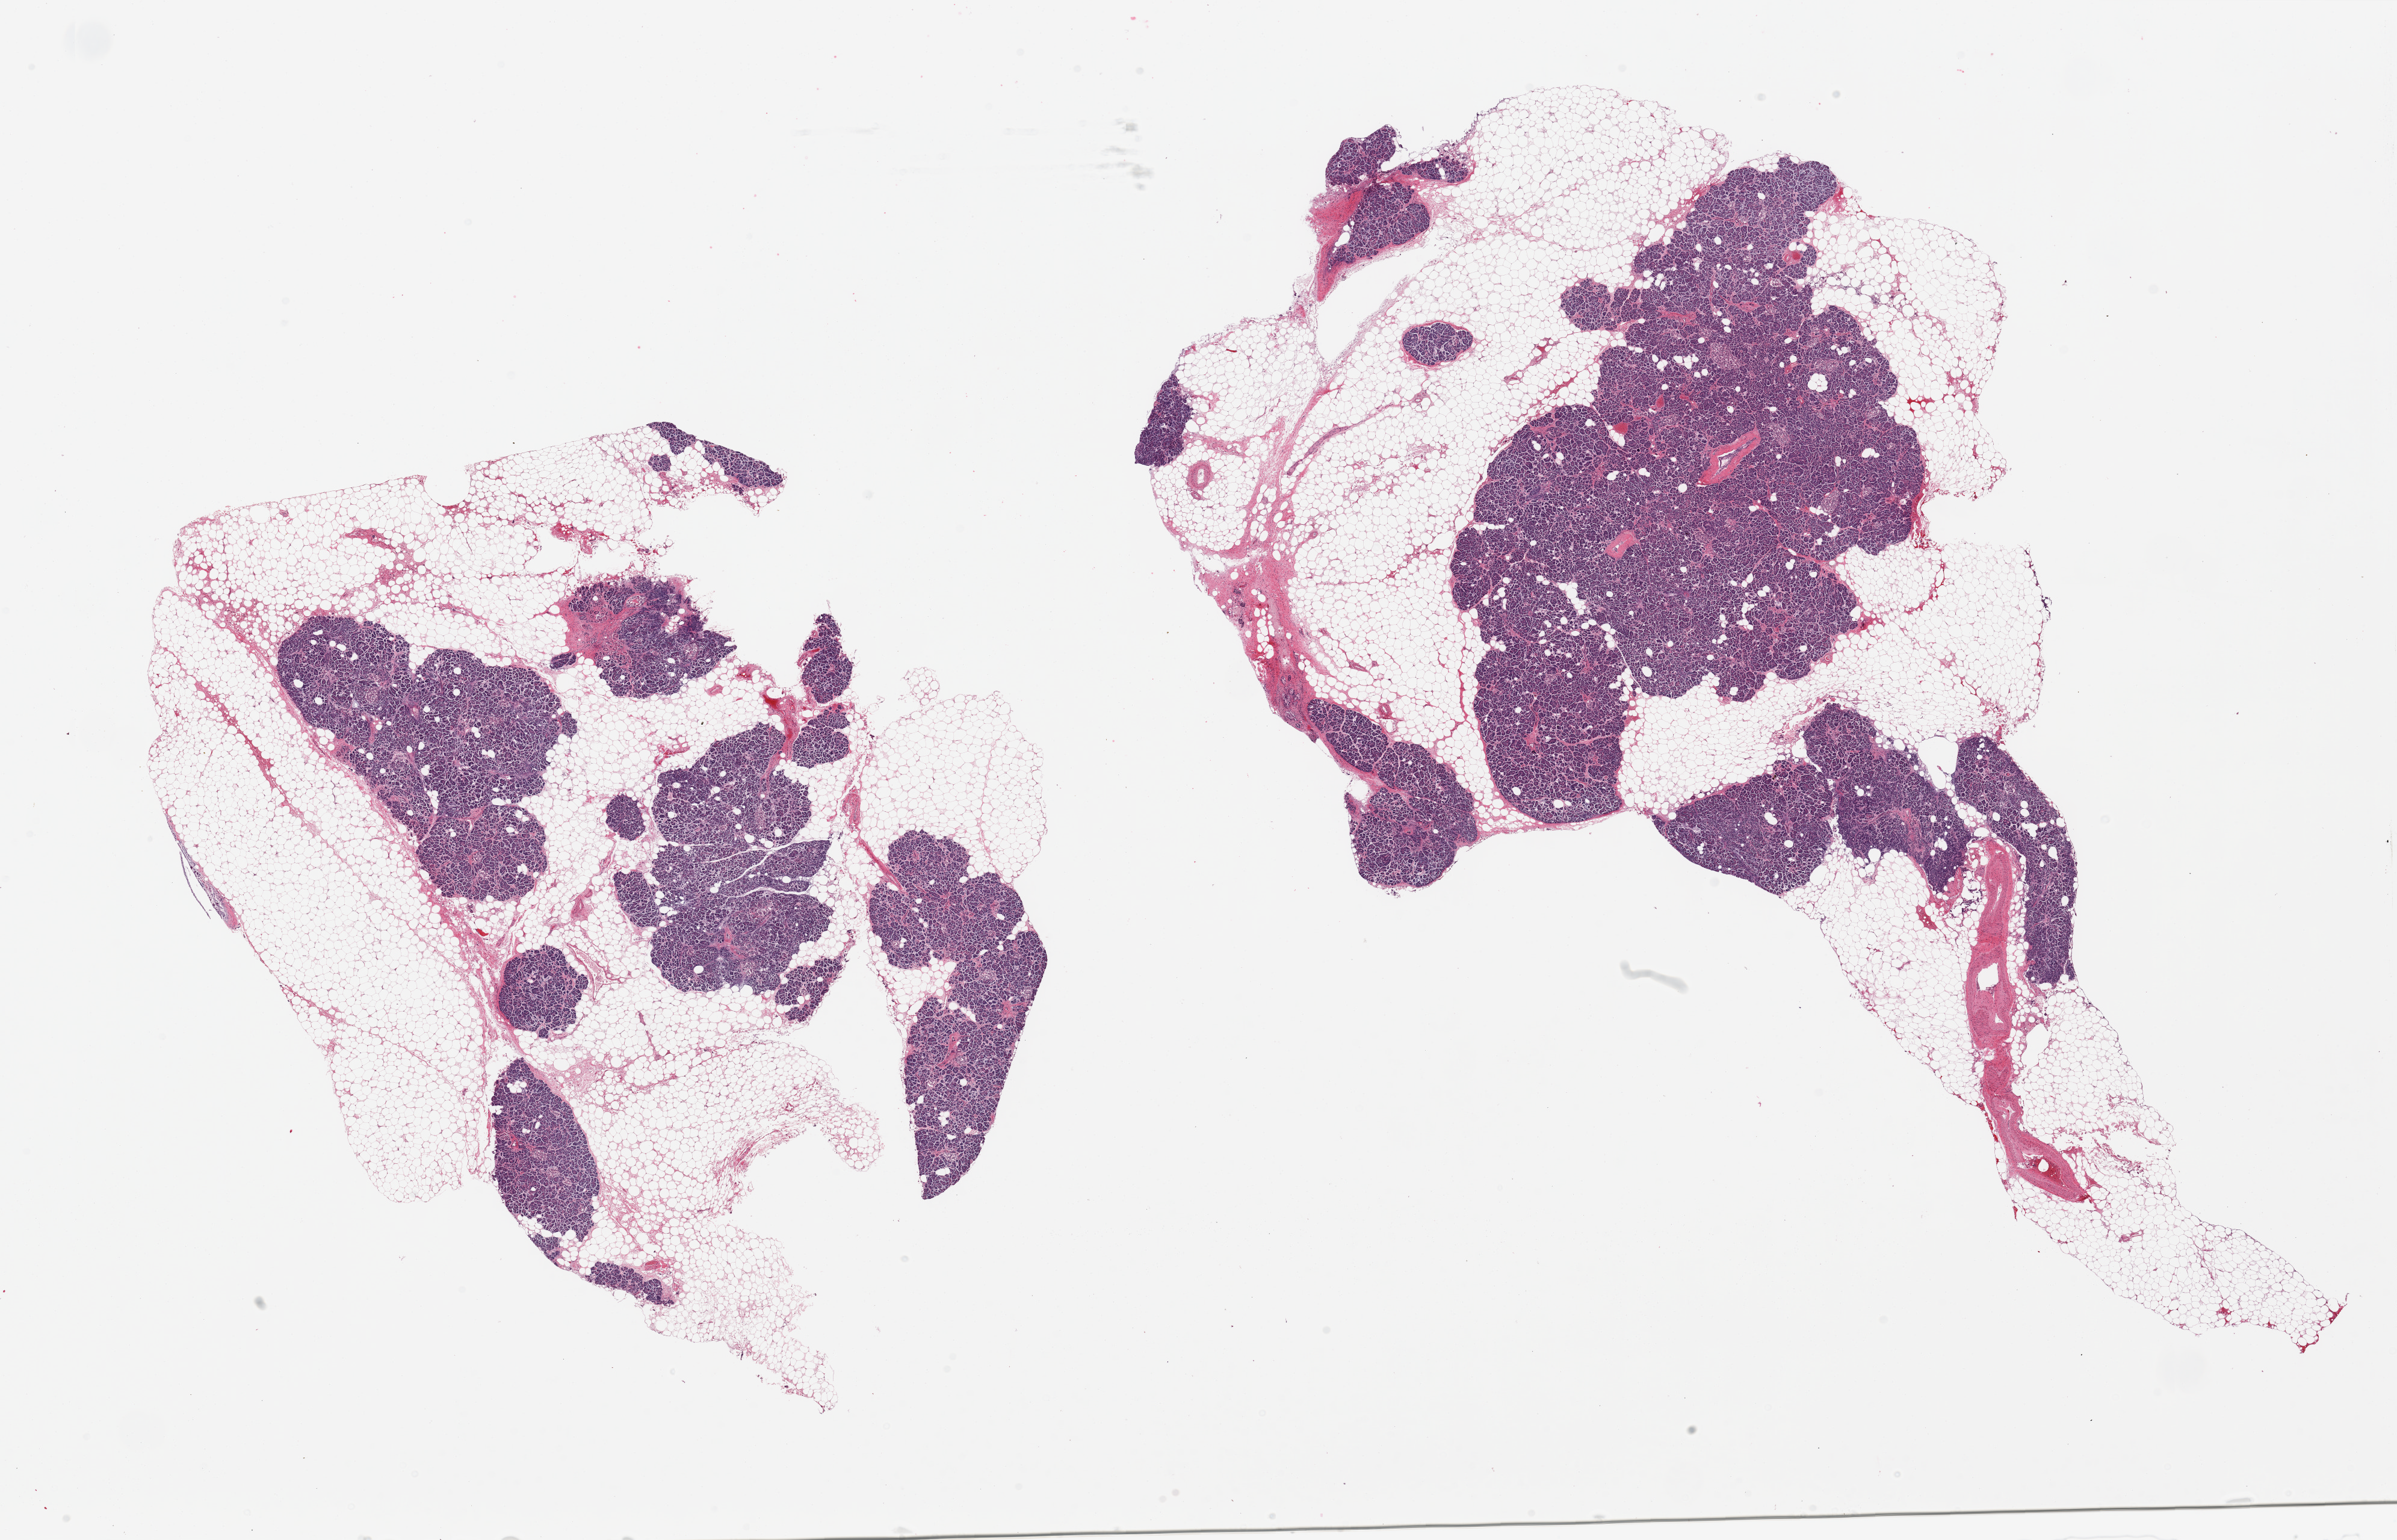
Digitized H&E-stained section, shown as a low-resolution overview of the whole scanned area (about 31.5 x 20.2 mm), PAXgene-fixed, paraffin-embedded tissue, target tissue: pancreas, tissue donor sample. Male donor.
Pathologist's review note for this sample: 2 pieces; 50% internal & external fat.